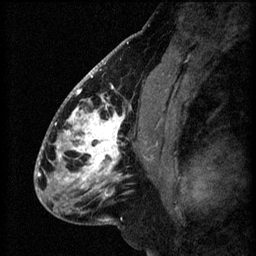
Breast MRI (dynamic contrast-enhanced), one sagittal slice; position 31 of 60 along the scan axis; 3 images stored at this slice position (order not interpretable as contrast timing); 1.5 T; TE 4.2 ms, TR 8.2 ms; 256 × 256 image matrix. Patient: female, 41 years.
Structures marked on this image (semi-automatically segmented with operator editing):
- analysis volume of interest (the breast-tissue region the enhancement analysis was run in; not a lesion): bounding box [x1, y1, x2, y2] px = [56, 104, 157, 207]
- tumour enhancement mask (voxels above the 70 % enhancement threshold inside the analysis volume of interest): [56, 104, 153, 197]